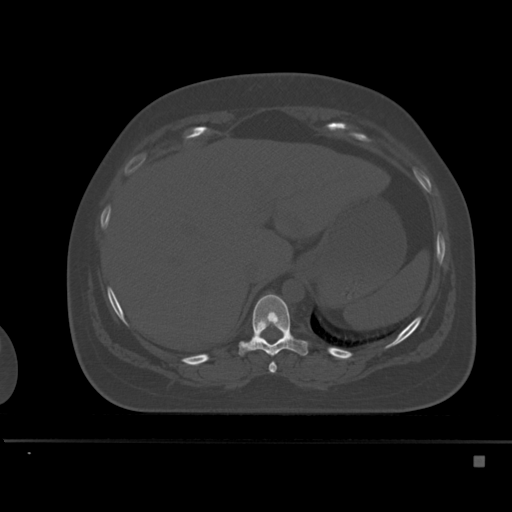
CT including the spine, one axial slice. Slice 248 of 495 in the series (ordered by position). Bone window (W 1800 / L 400 HU). 512 × 512 image matrix, field of view 404 × 404 mm. Female patient, age 33 years. From the clinical record (not read from this slice): primary cancer: breast.
Annotated regions visible in this slice (semi-automatic segmentation, software-assisted and operator-edited):
- T10 vertebra: bounding box (x1, y1, x2, y2) in pixels: (239, 294, 308, 356)
- T9 vertebra: (269, 362, 277, 373)